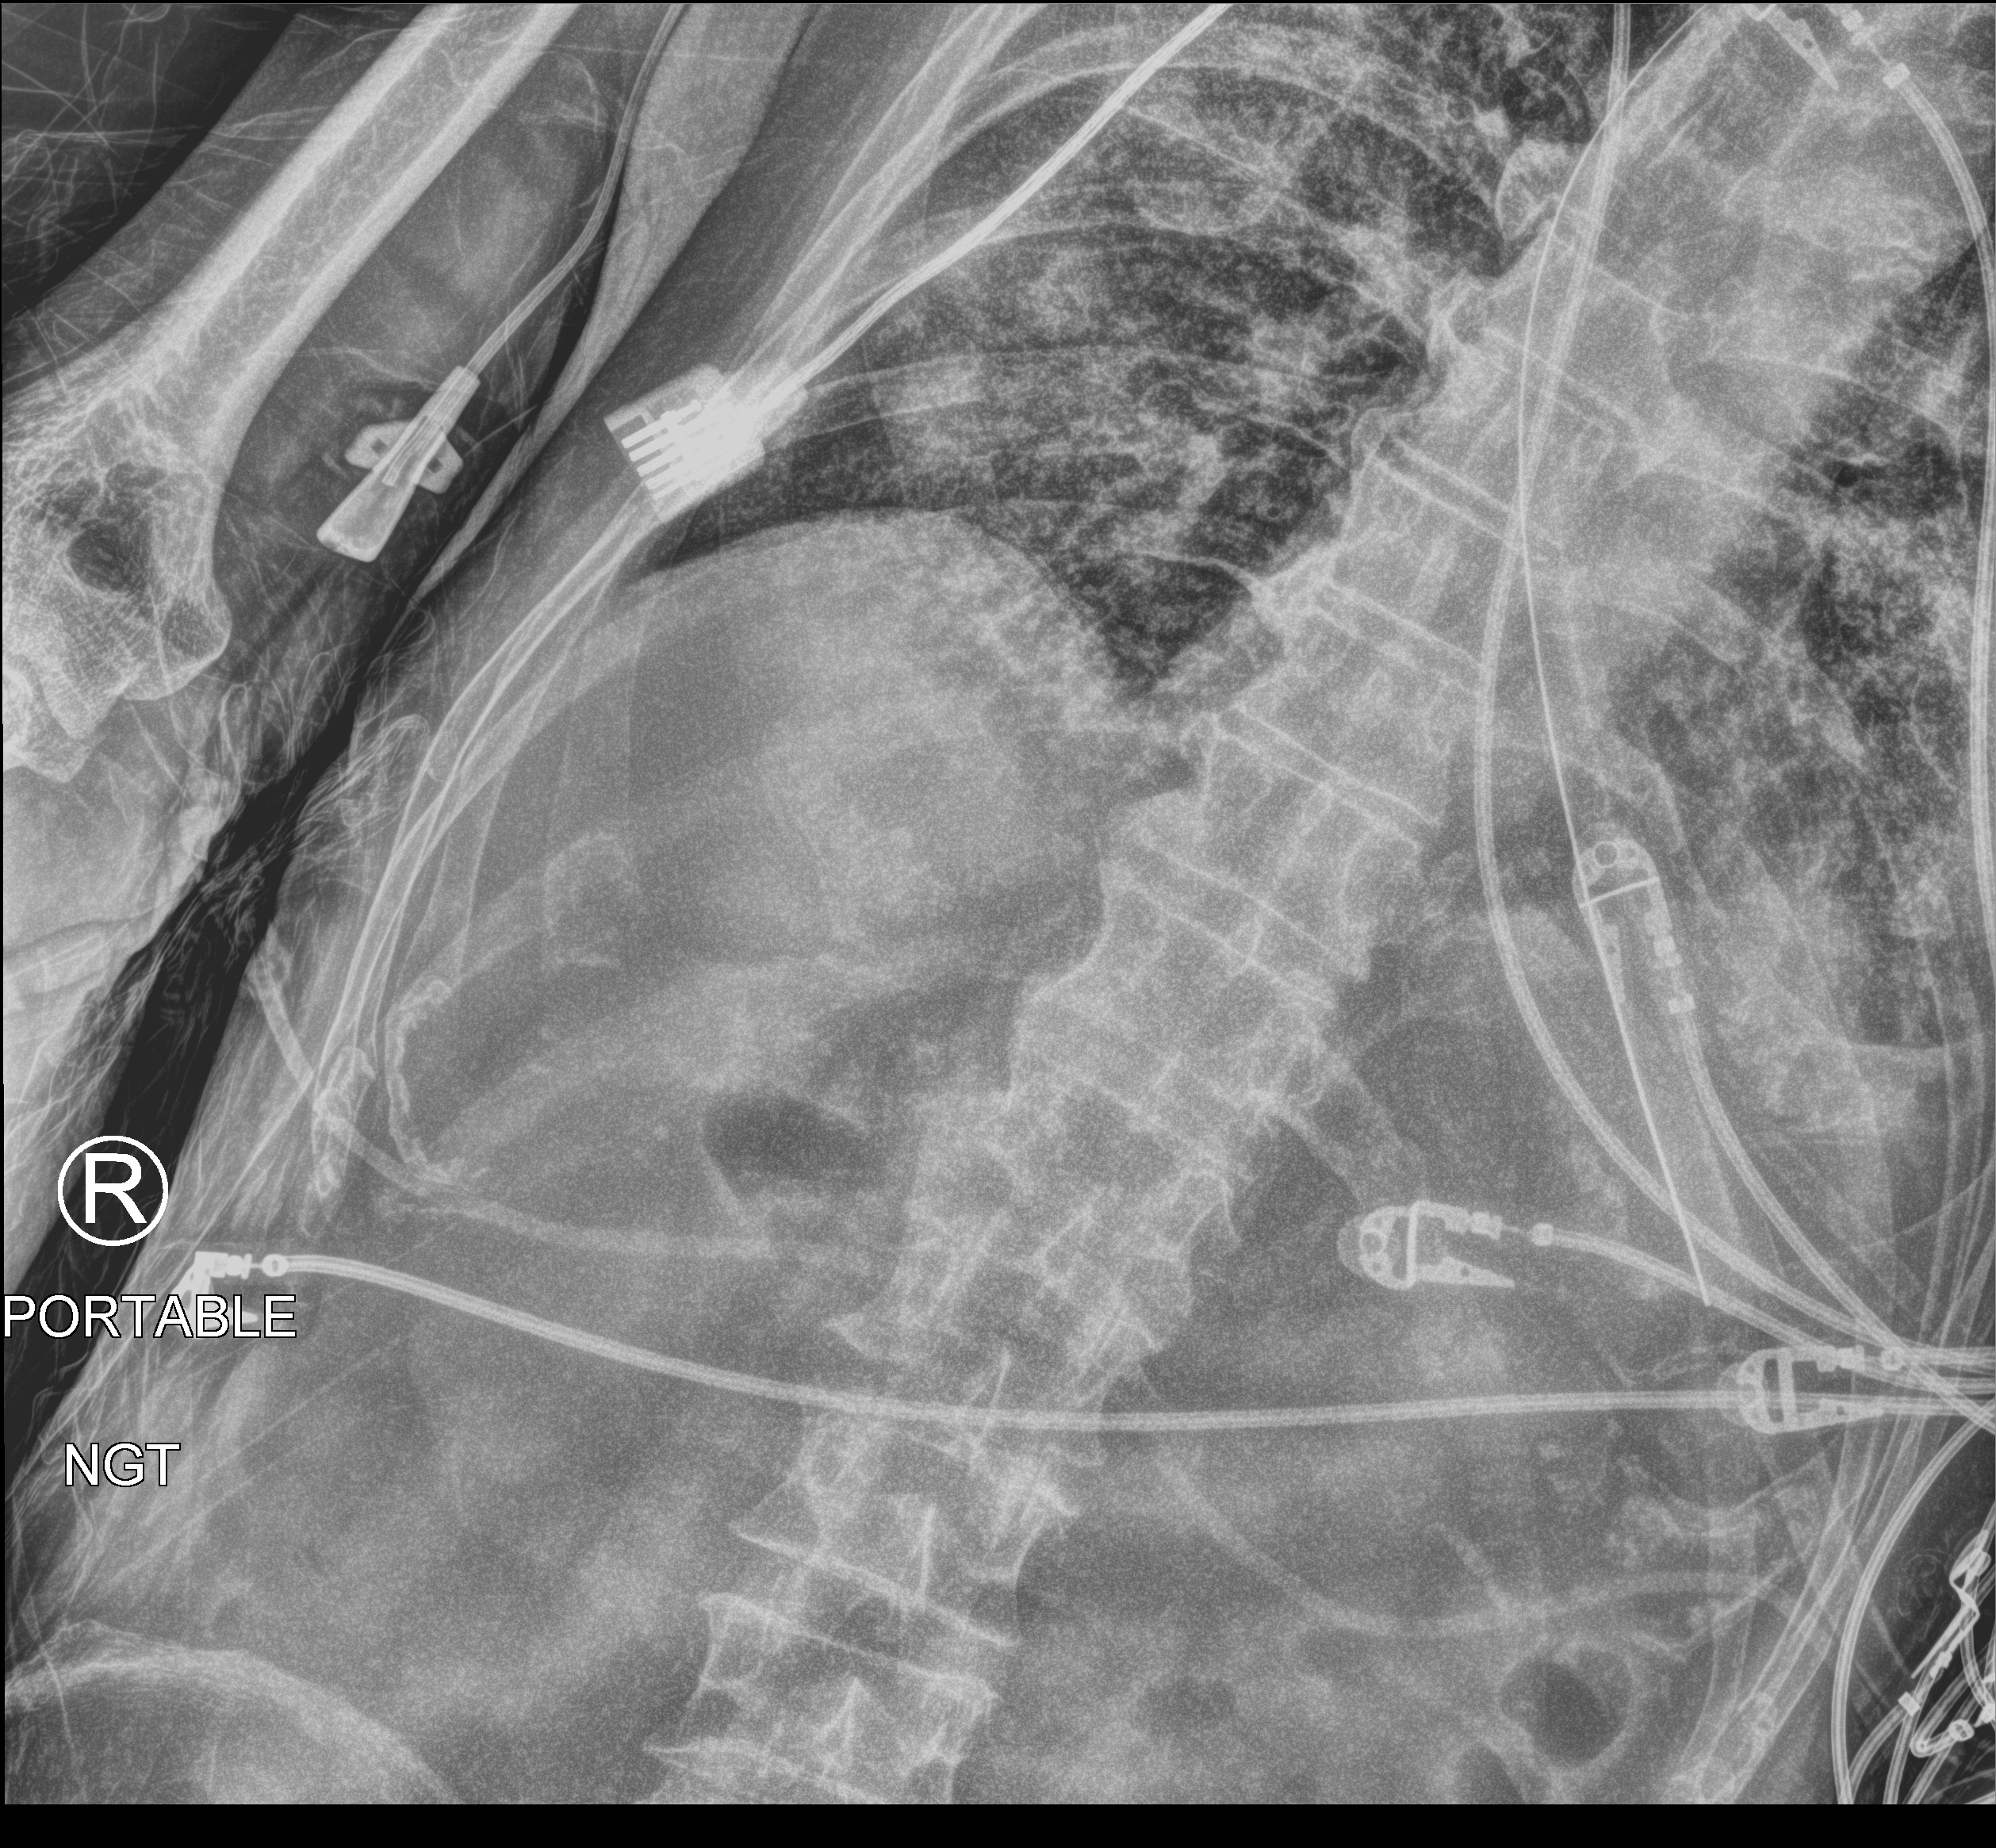
Bedside chest radiograph (computed radiography). Patient hospitalised with COVID-19; male, aged 60–74 years.
Hospital-stay facts (about this admission, not read from this image; timing relative to this image not recorded):
- COPD (admission record): no
- diabetes (admission record): yes
- hypertension (admission record): yes